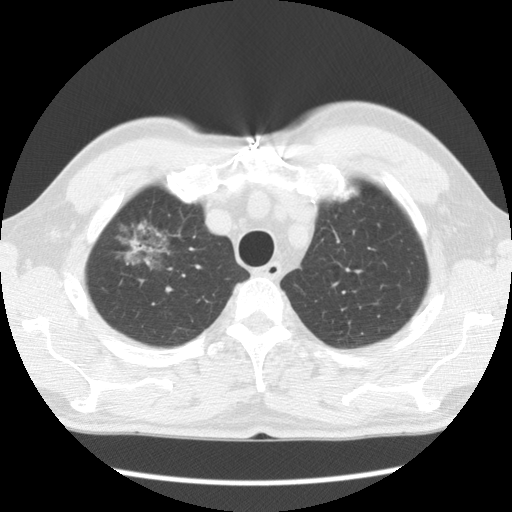
Chest CT (low-dose screening protocol), one axial image. First (baseline) screen. Lung window (W 1500 / L -600 HU). 2.5 mm slice thickness. Standard (soft-tissue) reconstruction kernel (STANDARD). 120 kVp. Slice 20 of 132 in the series. 512 × 512 image matrix, field of view 340 × 340 mm. Male, age 64 years at enrolment. Former smoker at enrolment.
Expert-annotated lung lesion, bounding box (x1, y1, x2, y2) in pixels: (101, 203, 176, 277). The screening reader recorded 2 non-calcified nodules or masses ≥4 mm on this exam (right upper lobe, left upper lobe); which of them this box marks is not recorded. Official screen result: positive, change unspecified: nodule(s) >= 4 mm or enlarging nodule(s), mass(es), or other non-specific abnormalities suspicious for lung cancer. Participant outcome: lung cancer diagnosed 750 days after this screen — adenocarcinoma, NOS, right upper lobe, well differentiated (G1), stage IB (AJCC 6th edition), 45 mm at pathology.